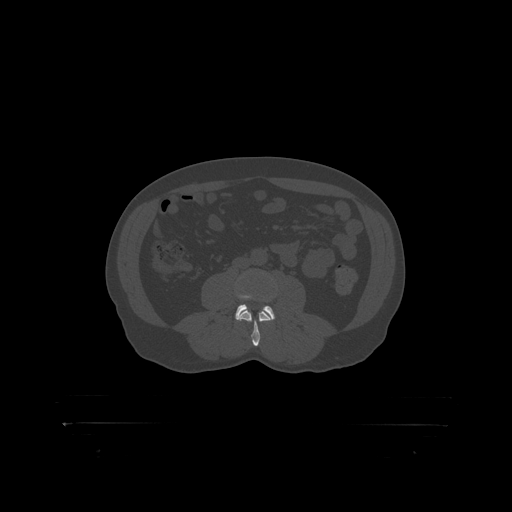
CT including the spine, one axial slice; slice 252 of 399 in the series (ordered by position); reconstruction kernel STANDARD; bone window (W 1800 / L 400 HU); 1.25 mm slice thickness; 512 × 512 image matrix. Male patient, age 46 years. From the clinical record (not read from this slice): primary cancer: skin.
Structures marked on this image (semi-automatic segmentation, software-assisted and operator-edited):
- L3 vertebra: bounding box (x1, y1, x2, y2) in pixels: (240, 309, 269, 319)
- L4 vertebra: (236, 295, 275, 317)